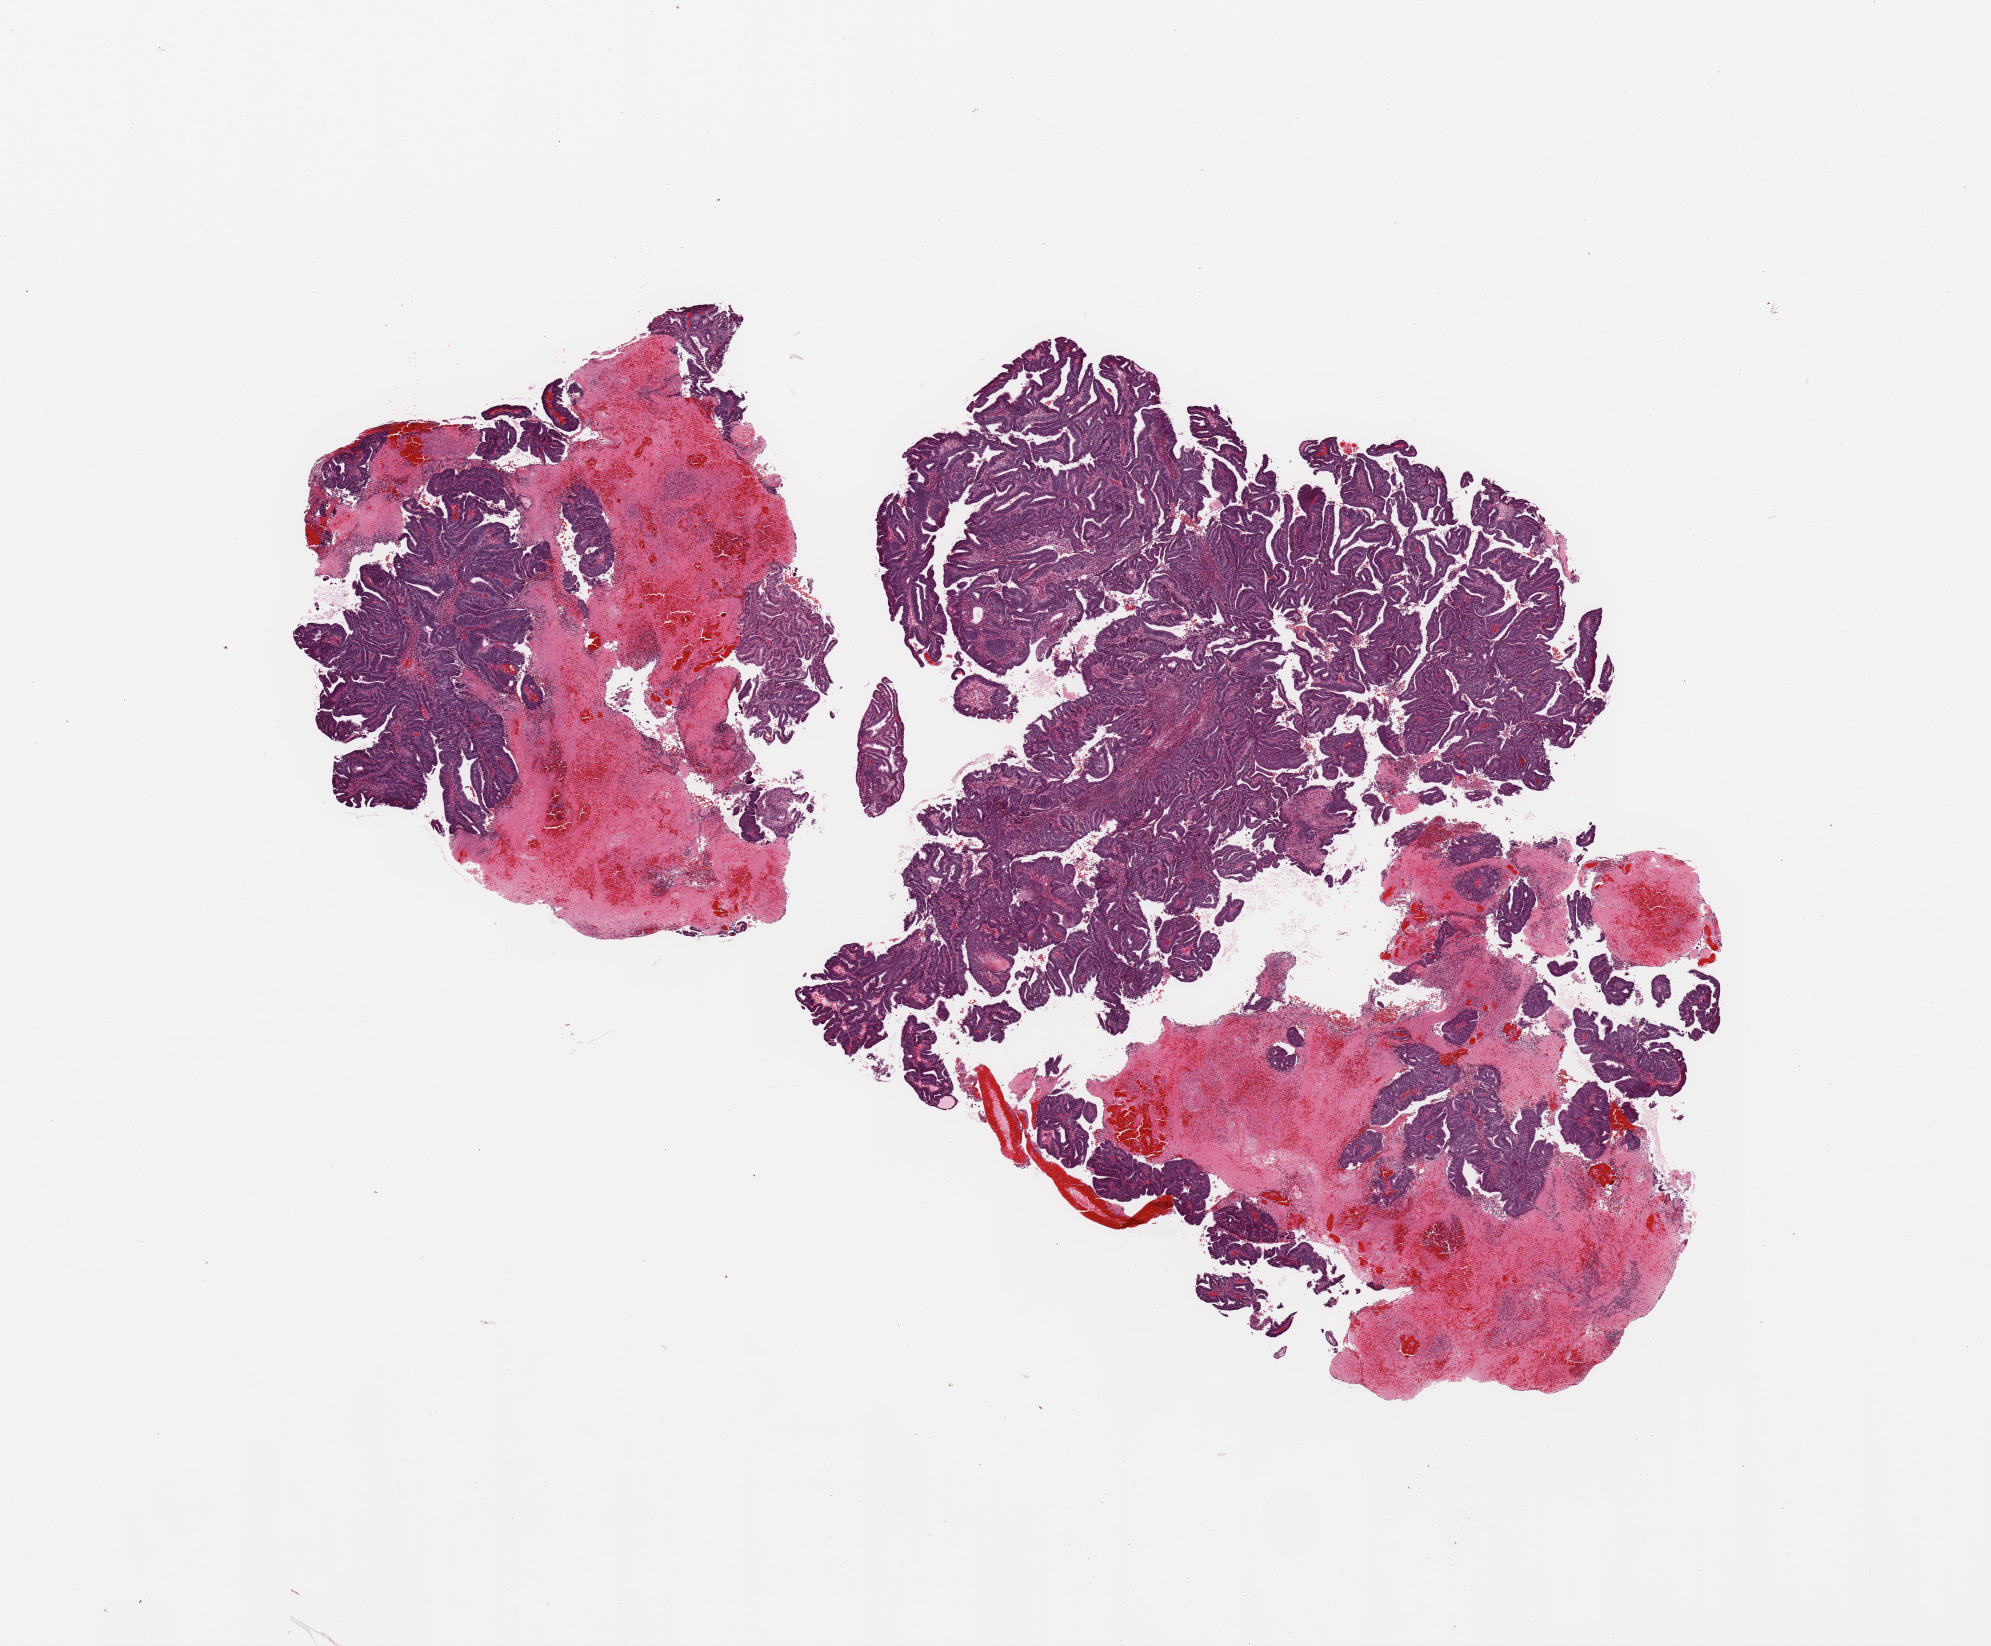
Whole-slide histology image, Hematoxylin and eosin (H&E) stained — shown as a low-resolution overview of the whole scanned area (about 15.8 x 13.0 mm, from a 20x scan), tumour tissue sample, sampled site: uterus. 57-year-old female patient. Histologic grade: G1 (well differentiated). Composition of this section per pathologist review: tumour nuclei 90%, necrosis 0%.
Histologic diagnosis: Endometrioid adenocarcinoma, NOS. AJCC pathologic stage: I.